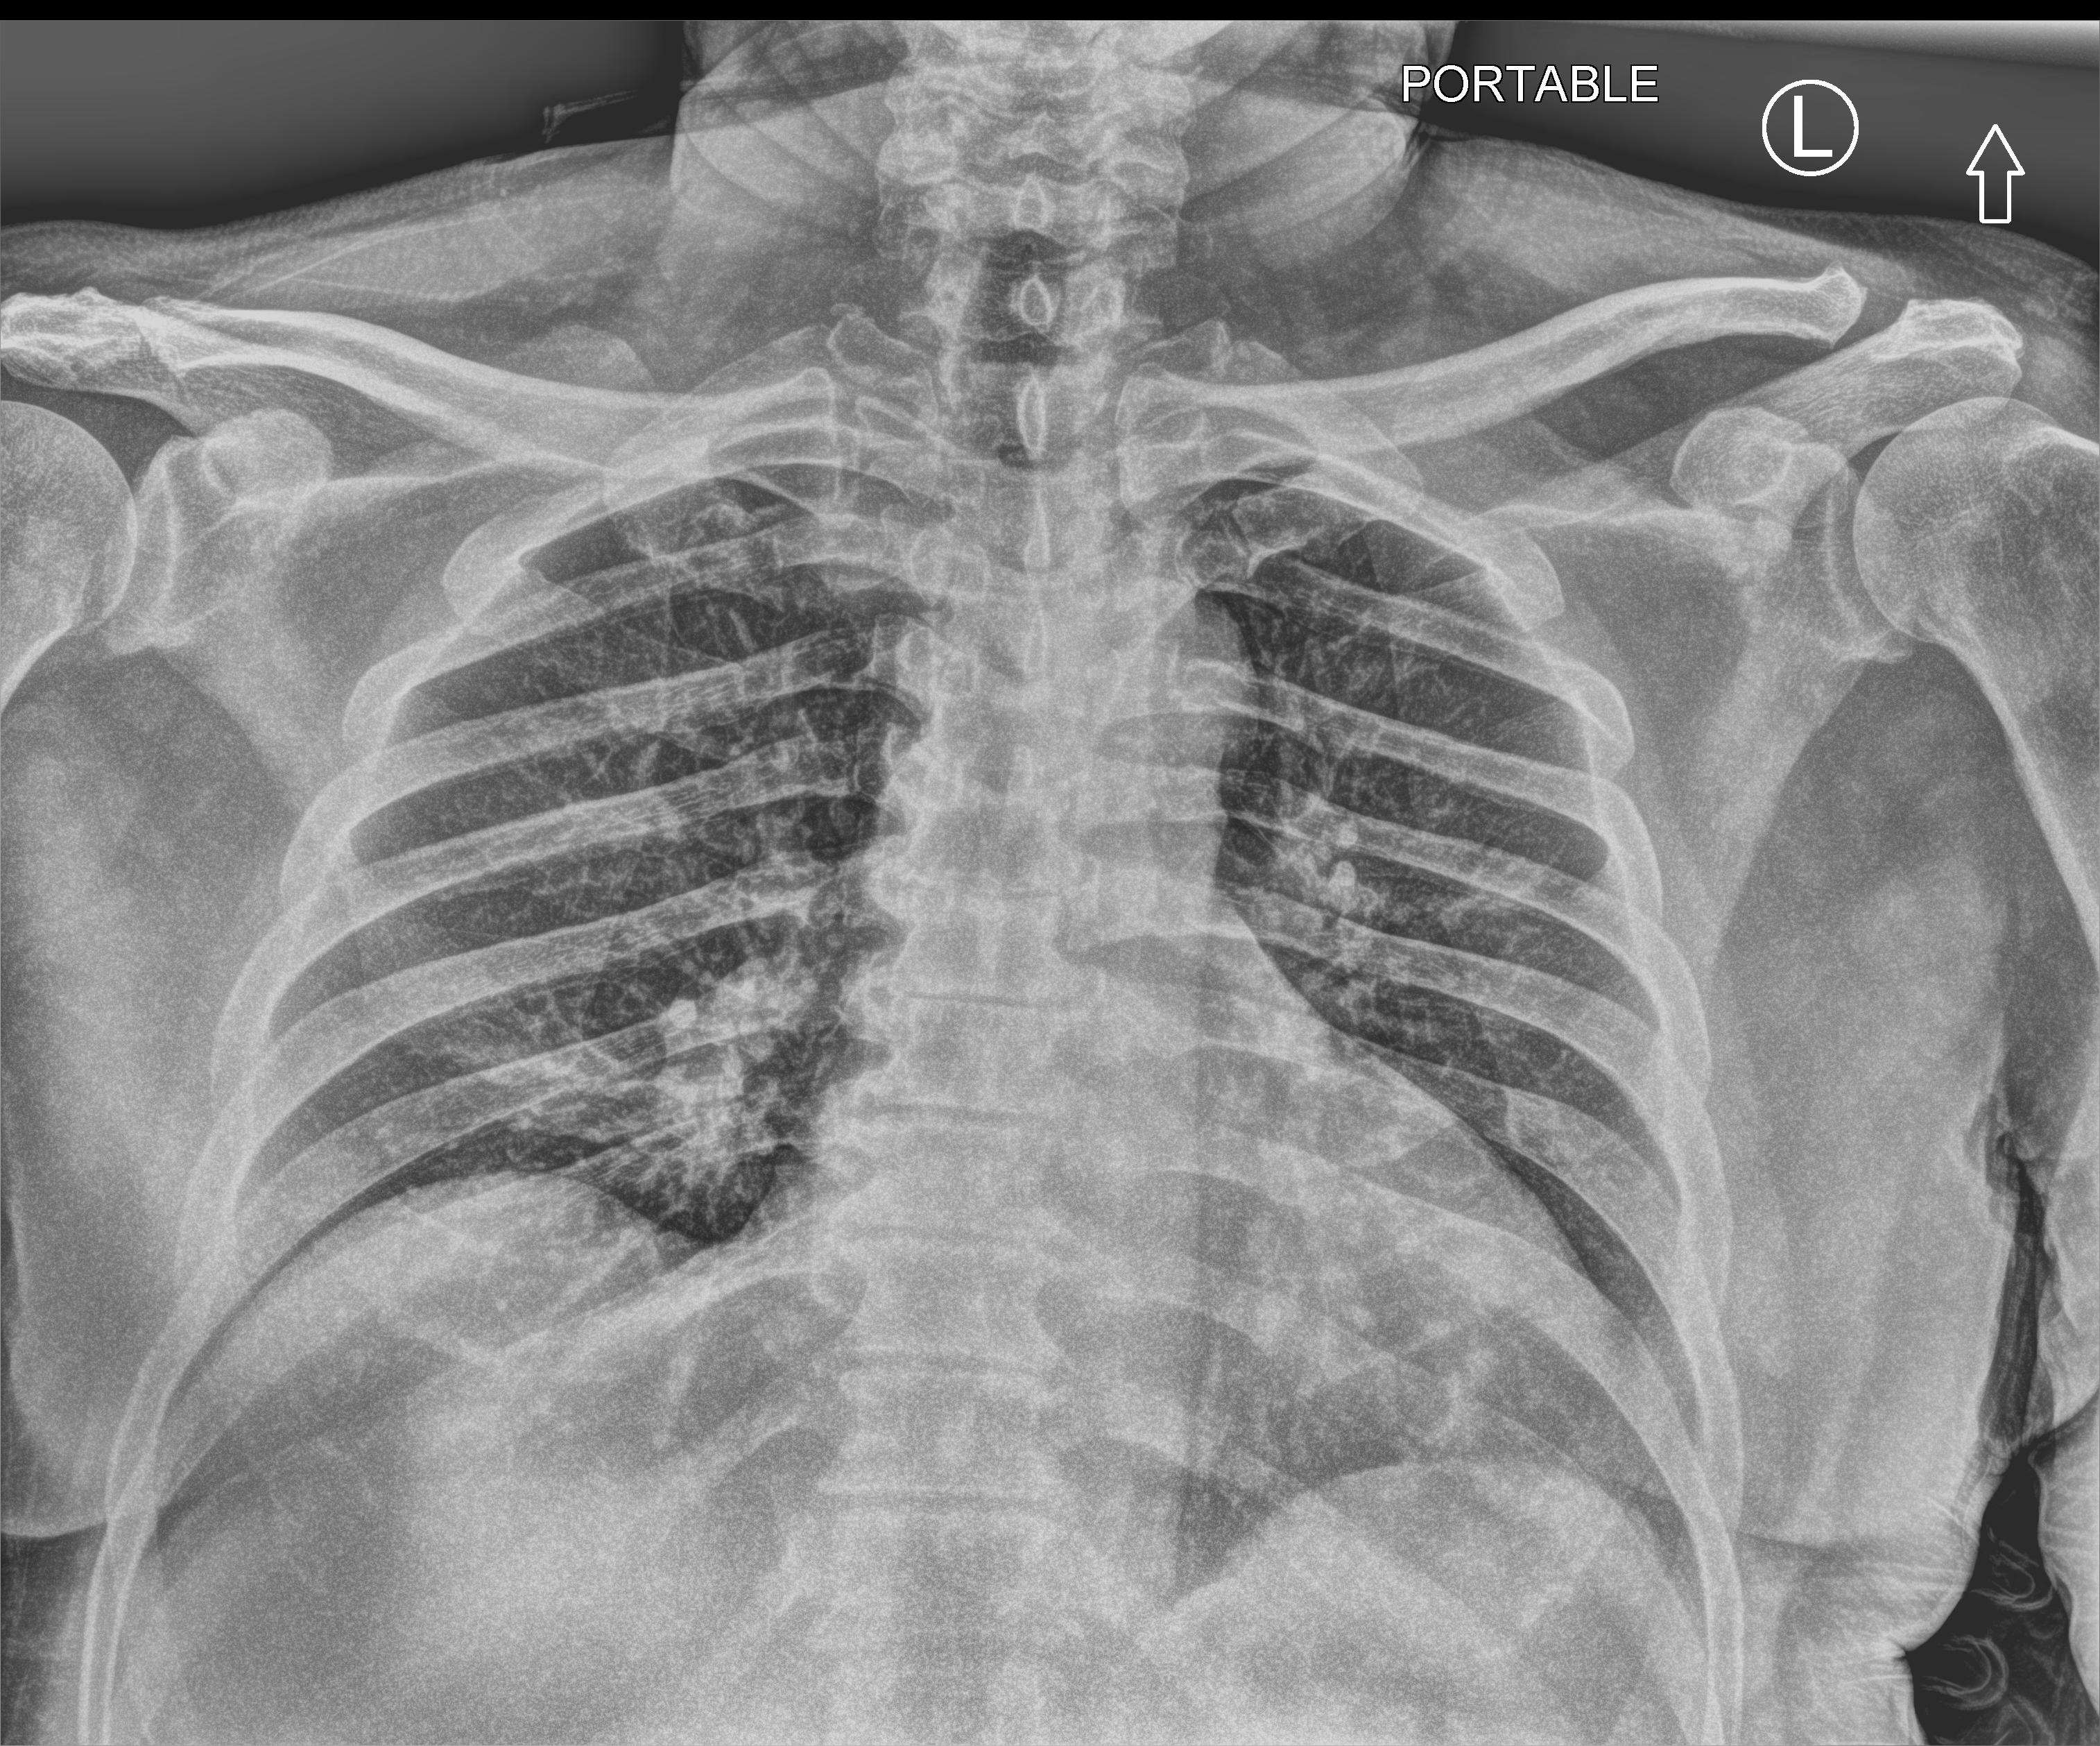
Bedside chest radiograph (computed radiography), anteroposterior (AP) projection. Male patient hospitalised with COVID-19, age 60–74 years.
Hospital-stay facts (about this admission, not read from this image; timing relative to this image not recorded): hypertension (admission record): yes.